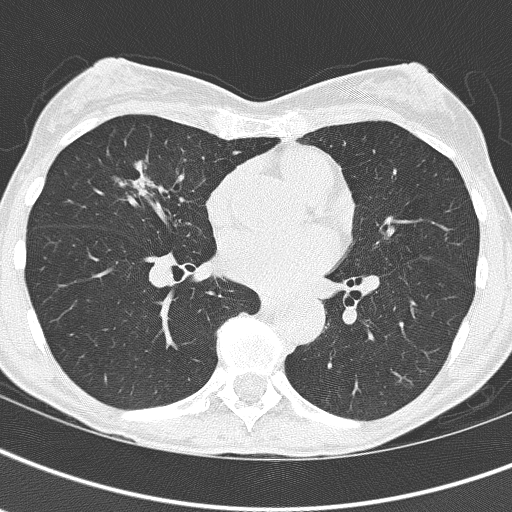
Axial slice from a low-dose chest CT screening exam, first (baseline) screen, lung window (W 1500 / L -600 HU), 2 mm slice thickness, lung (sharp) reconstruction kernel (B60f), slice 89 of 161 in the series, 512 × 512 image matrix. Female participant, aged 67 years at enrolment. Current smoker at enrolment.
Expert reader's lesion annotation, bounding box (x1, y1, x2, y2) in pixels: (91, 141, 174, 220). No non-calcified nodule or mass ≥4 mm was recorded by the screening reader at this exam. Lung cancer was diagnosed 832 days after this screen (after the third annual screen): bronchiolo-alveolar adenocarcinoma, NOS, right middle lobe, well differentiated (G1), stage IA (AJCC 6th edition), 25 mm at pathology.